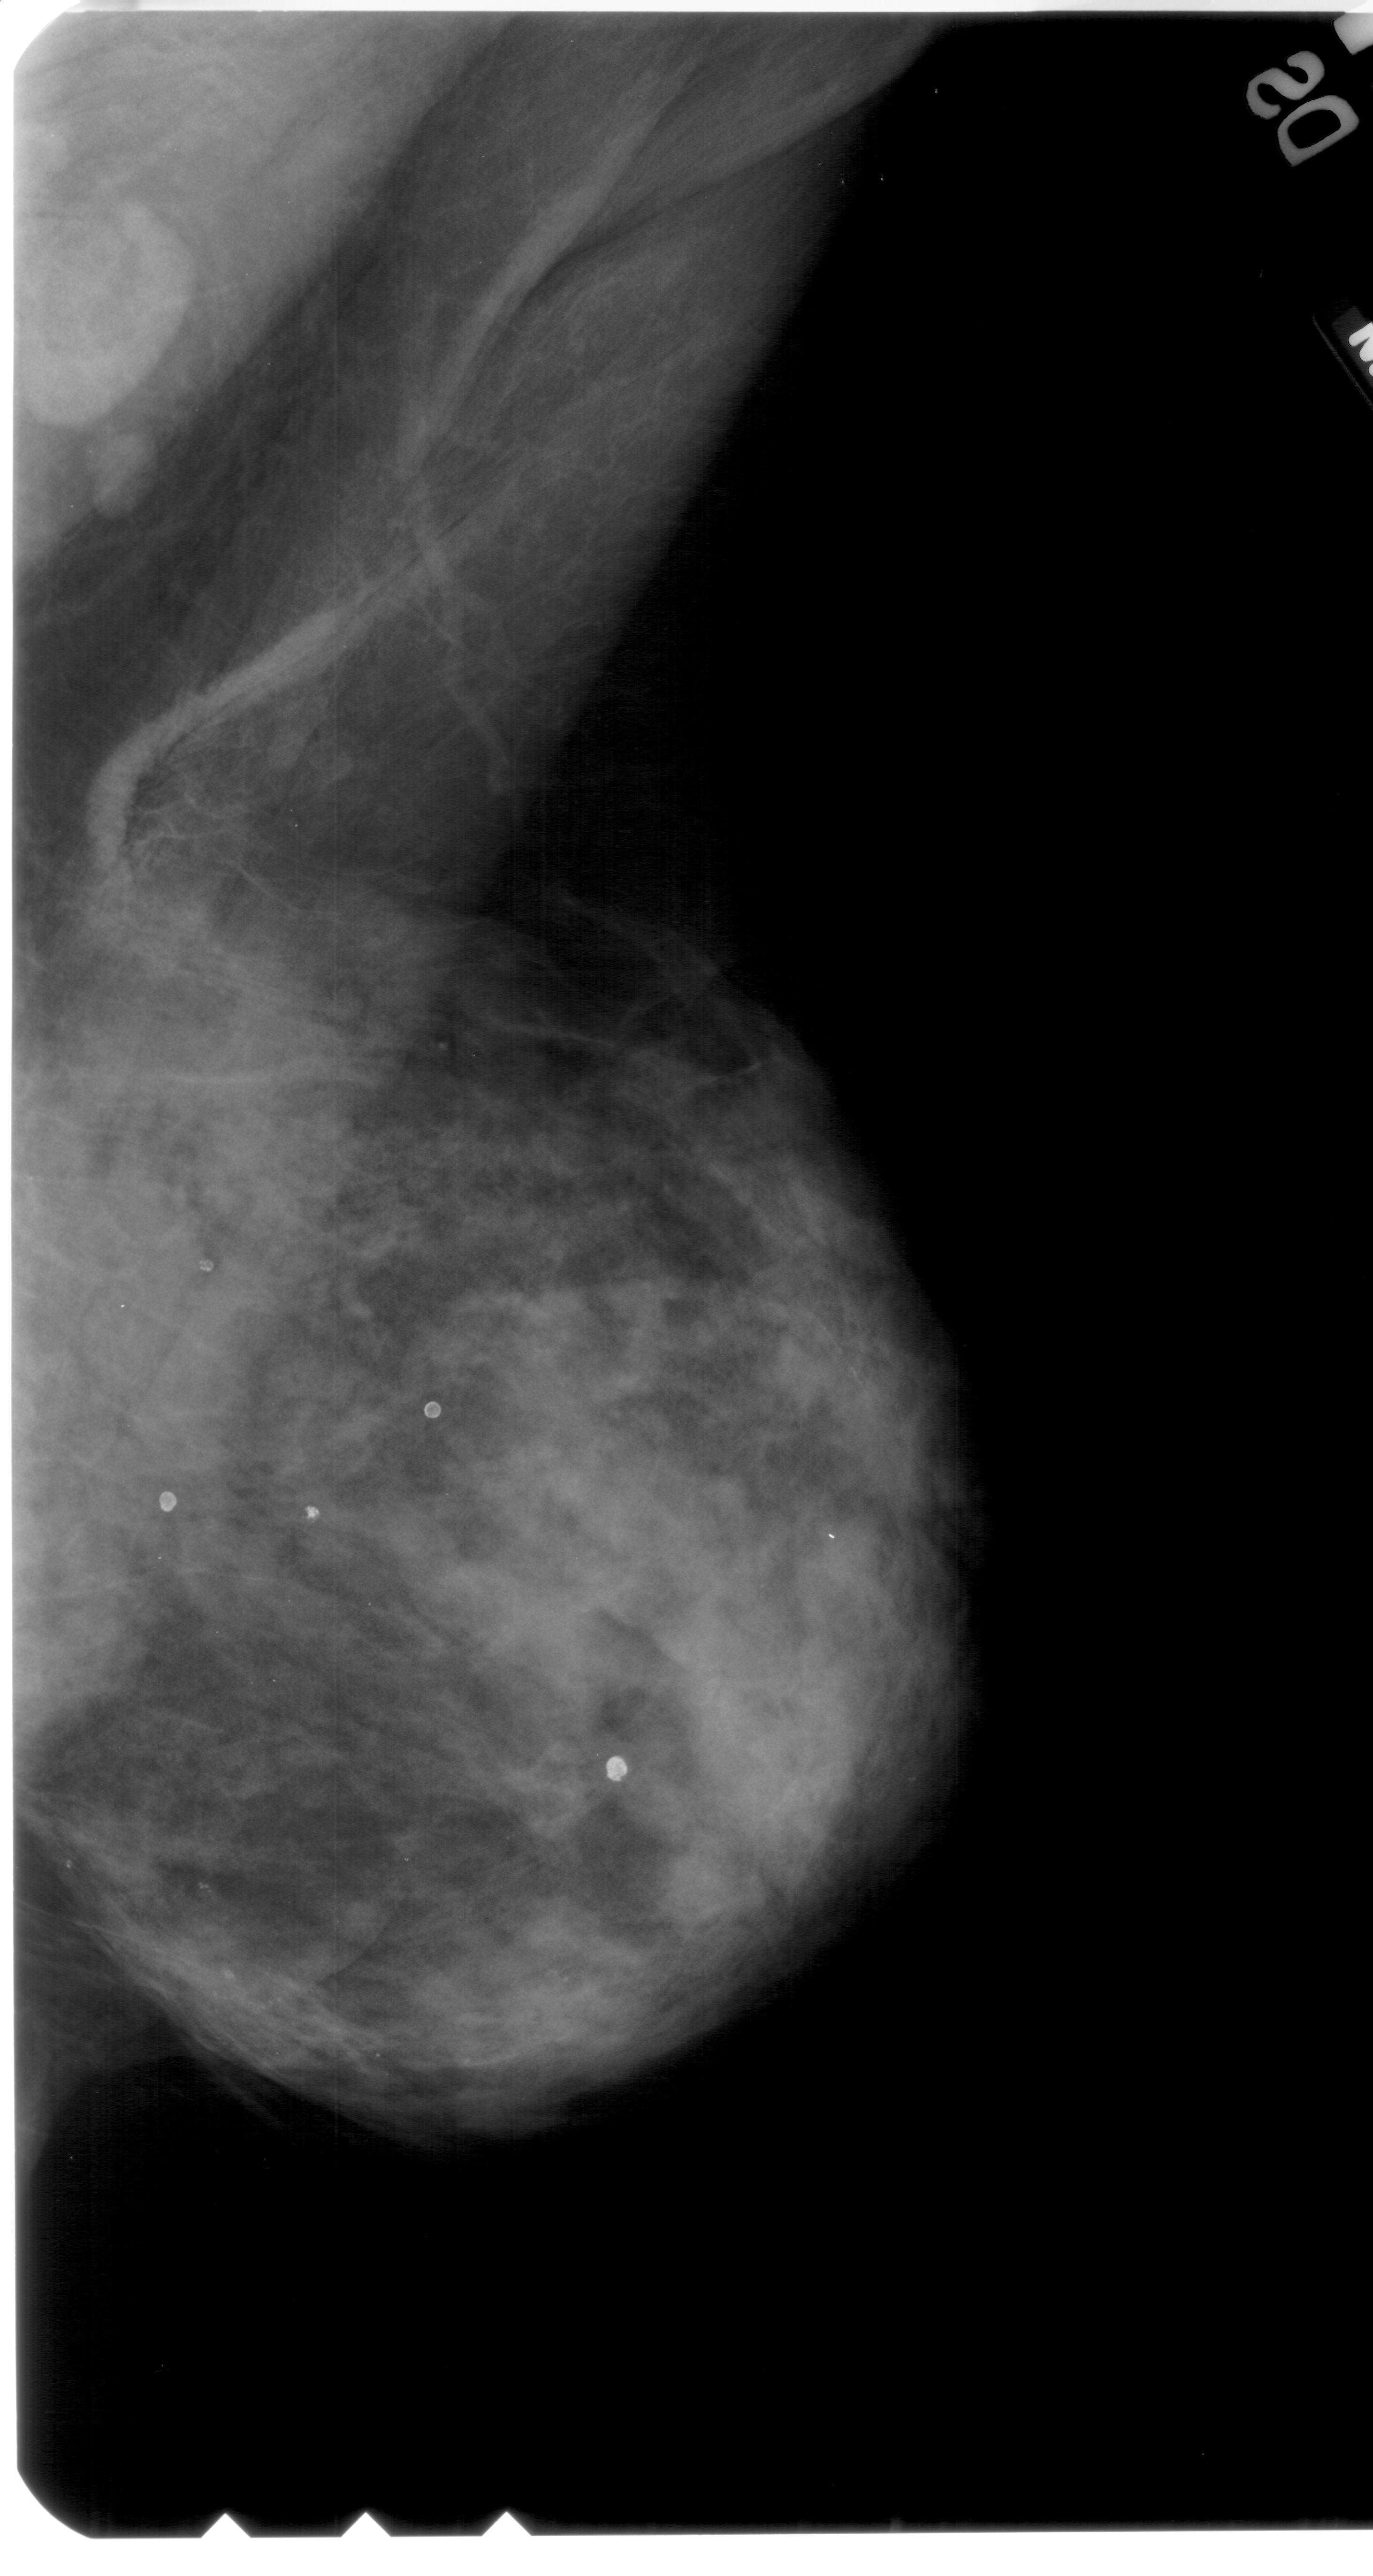
Scanned film-screen mammogram; right breast; mediolateral oblique (MLO) view; BI-RADS breast density category 4 (scale 1–4).
- Abnormality record for this image: calcifications, morphology pleomorphic, distribution clustered; BI-RADS assessment category 4; subtlety rating 2 on a 1 (subtle) to 5 (obvious) scale; pathology result (as recorded, not read from the image): benign.